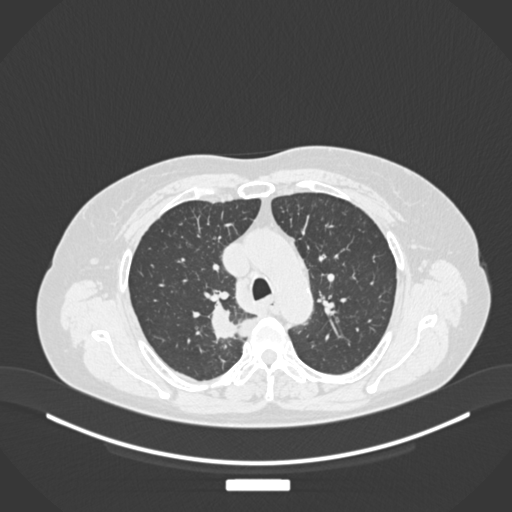
Chest CT, one axial slice; slice 184 of 237 in the series (ordered by position); reconstruction kernel B30f; 120 kVp; lung window (W 1500 / L -600 HU); 1 mm slice thickness; 512 × 512 image matrix, field of view 400 × 400 mm. Patient: female, 62 years. Case-level facts recorded for this patient, not image findings: clinical TNM (as recorded): T1c N1 M0.
Structures marked on this image (rectangle marked by the reading radiologist):
- lung tumour (recorded histology: squamous cell carcinoma): bounding box [x1, y1, x2, y2] px = [208, 299, 256, 344]